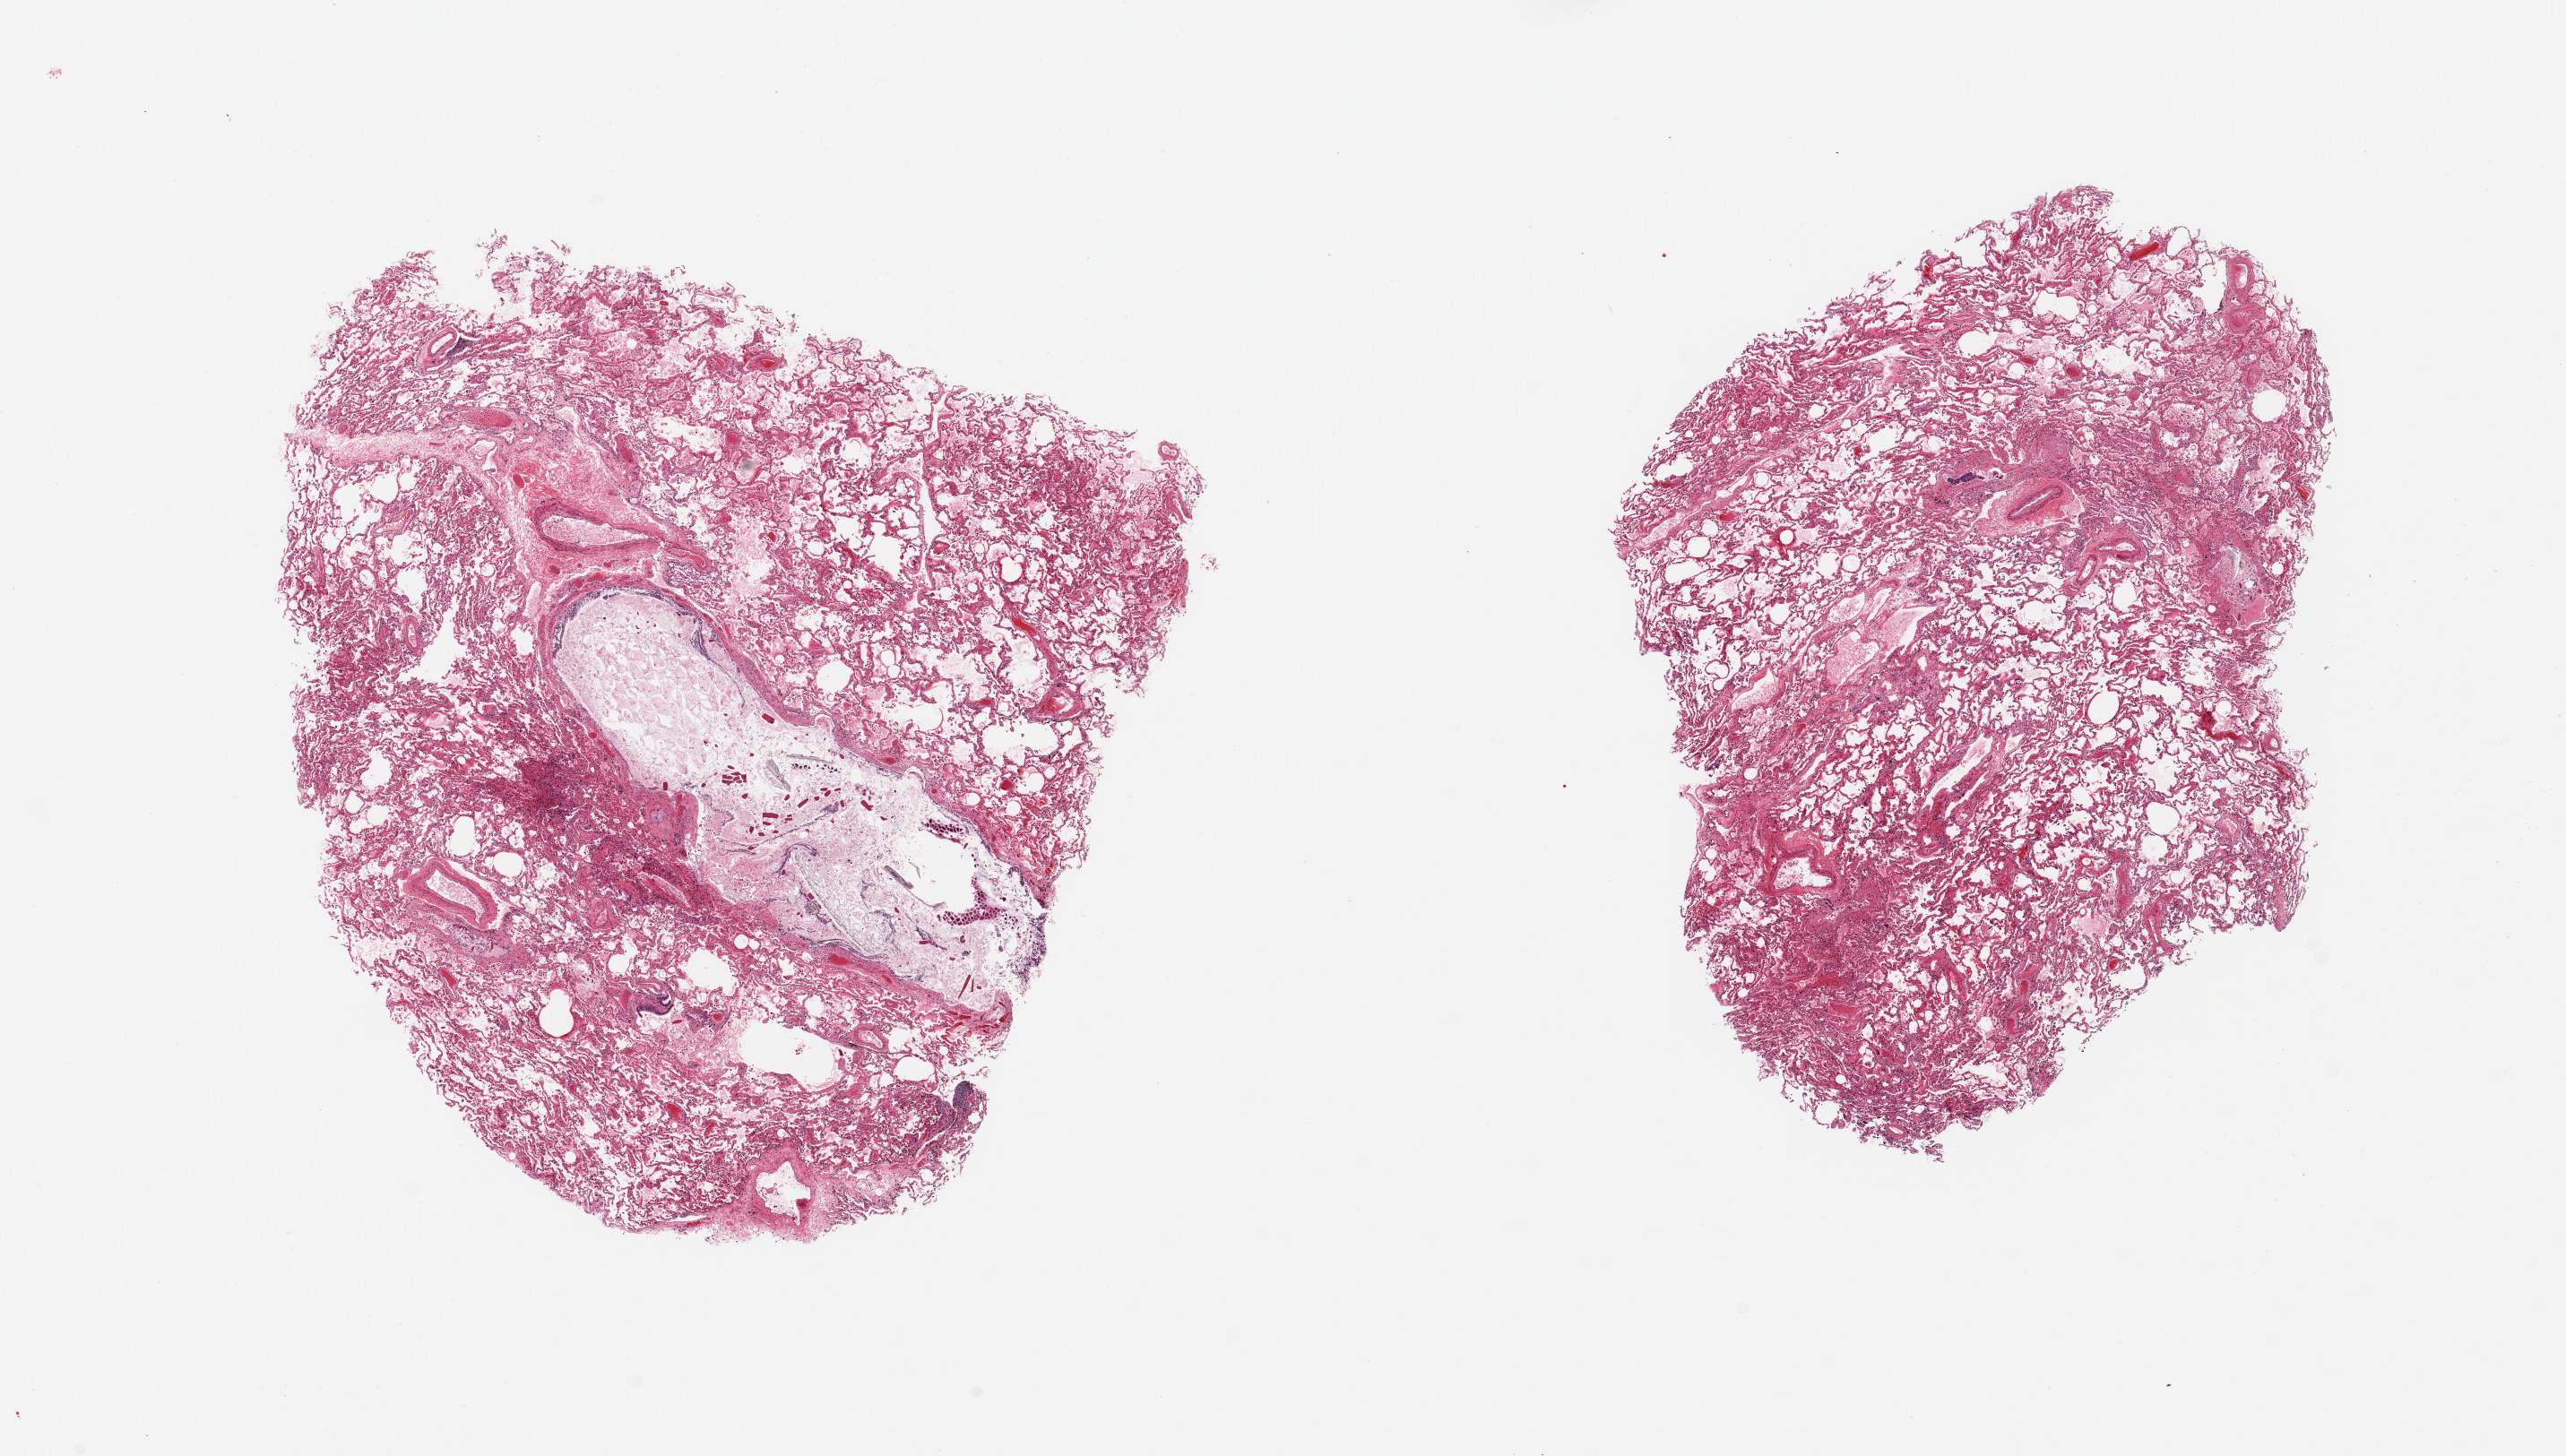
Digitized H&E-stained section, low-resolution overview of the scanned area, about 22.6 x 12.9 mm, PAXgene-fixed, paraffin-embedded tissue, target tissue: lung, tissue donor sample. Donor: male.
Pathologist's review note for this sample: 2 pieces, perimortem apsirated foreign material, vegetable/anlmal matter, delinetaed. No significant inflammatory reaction.